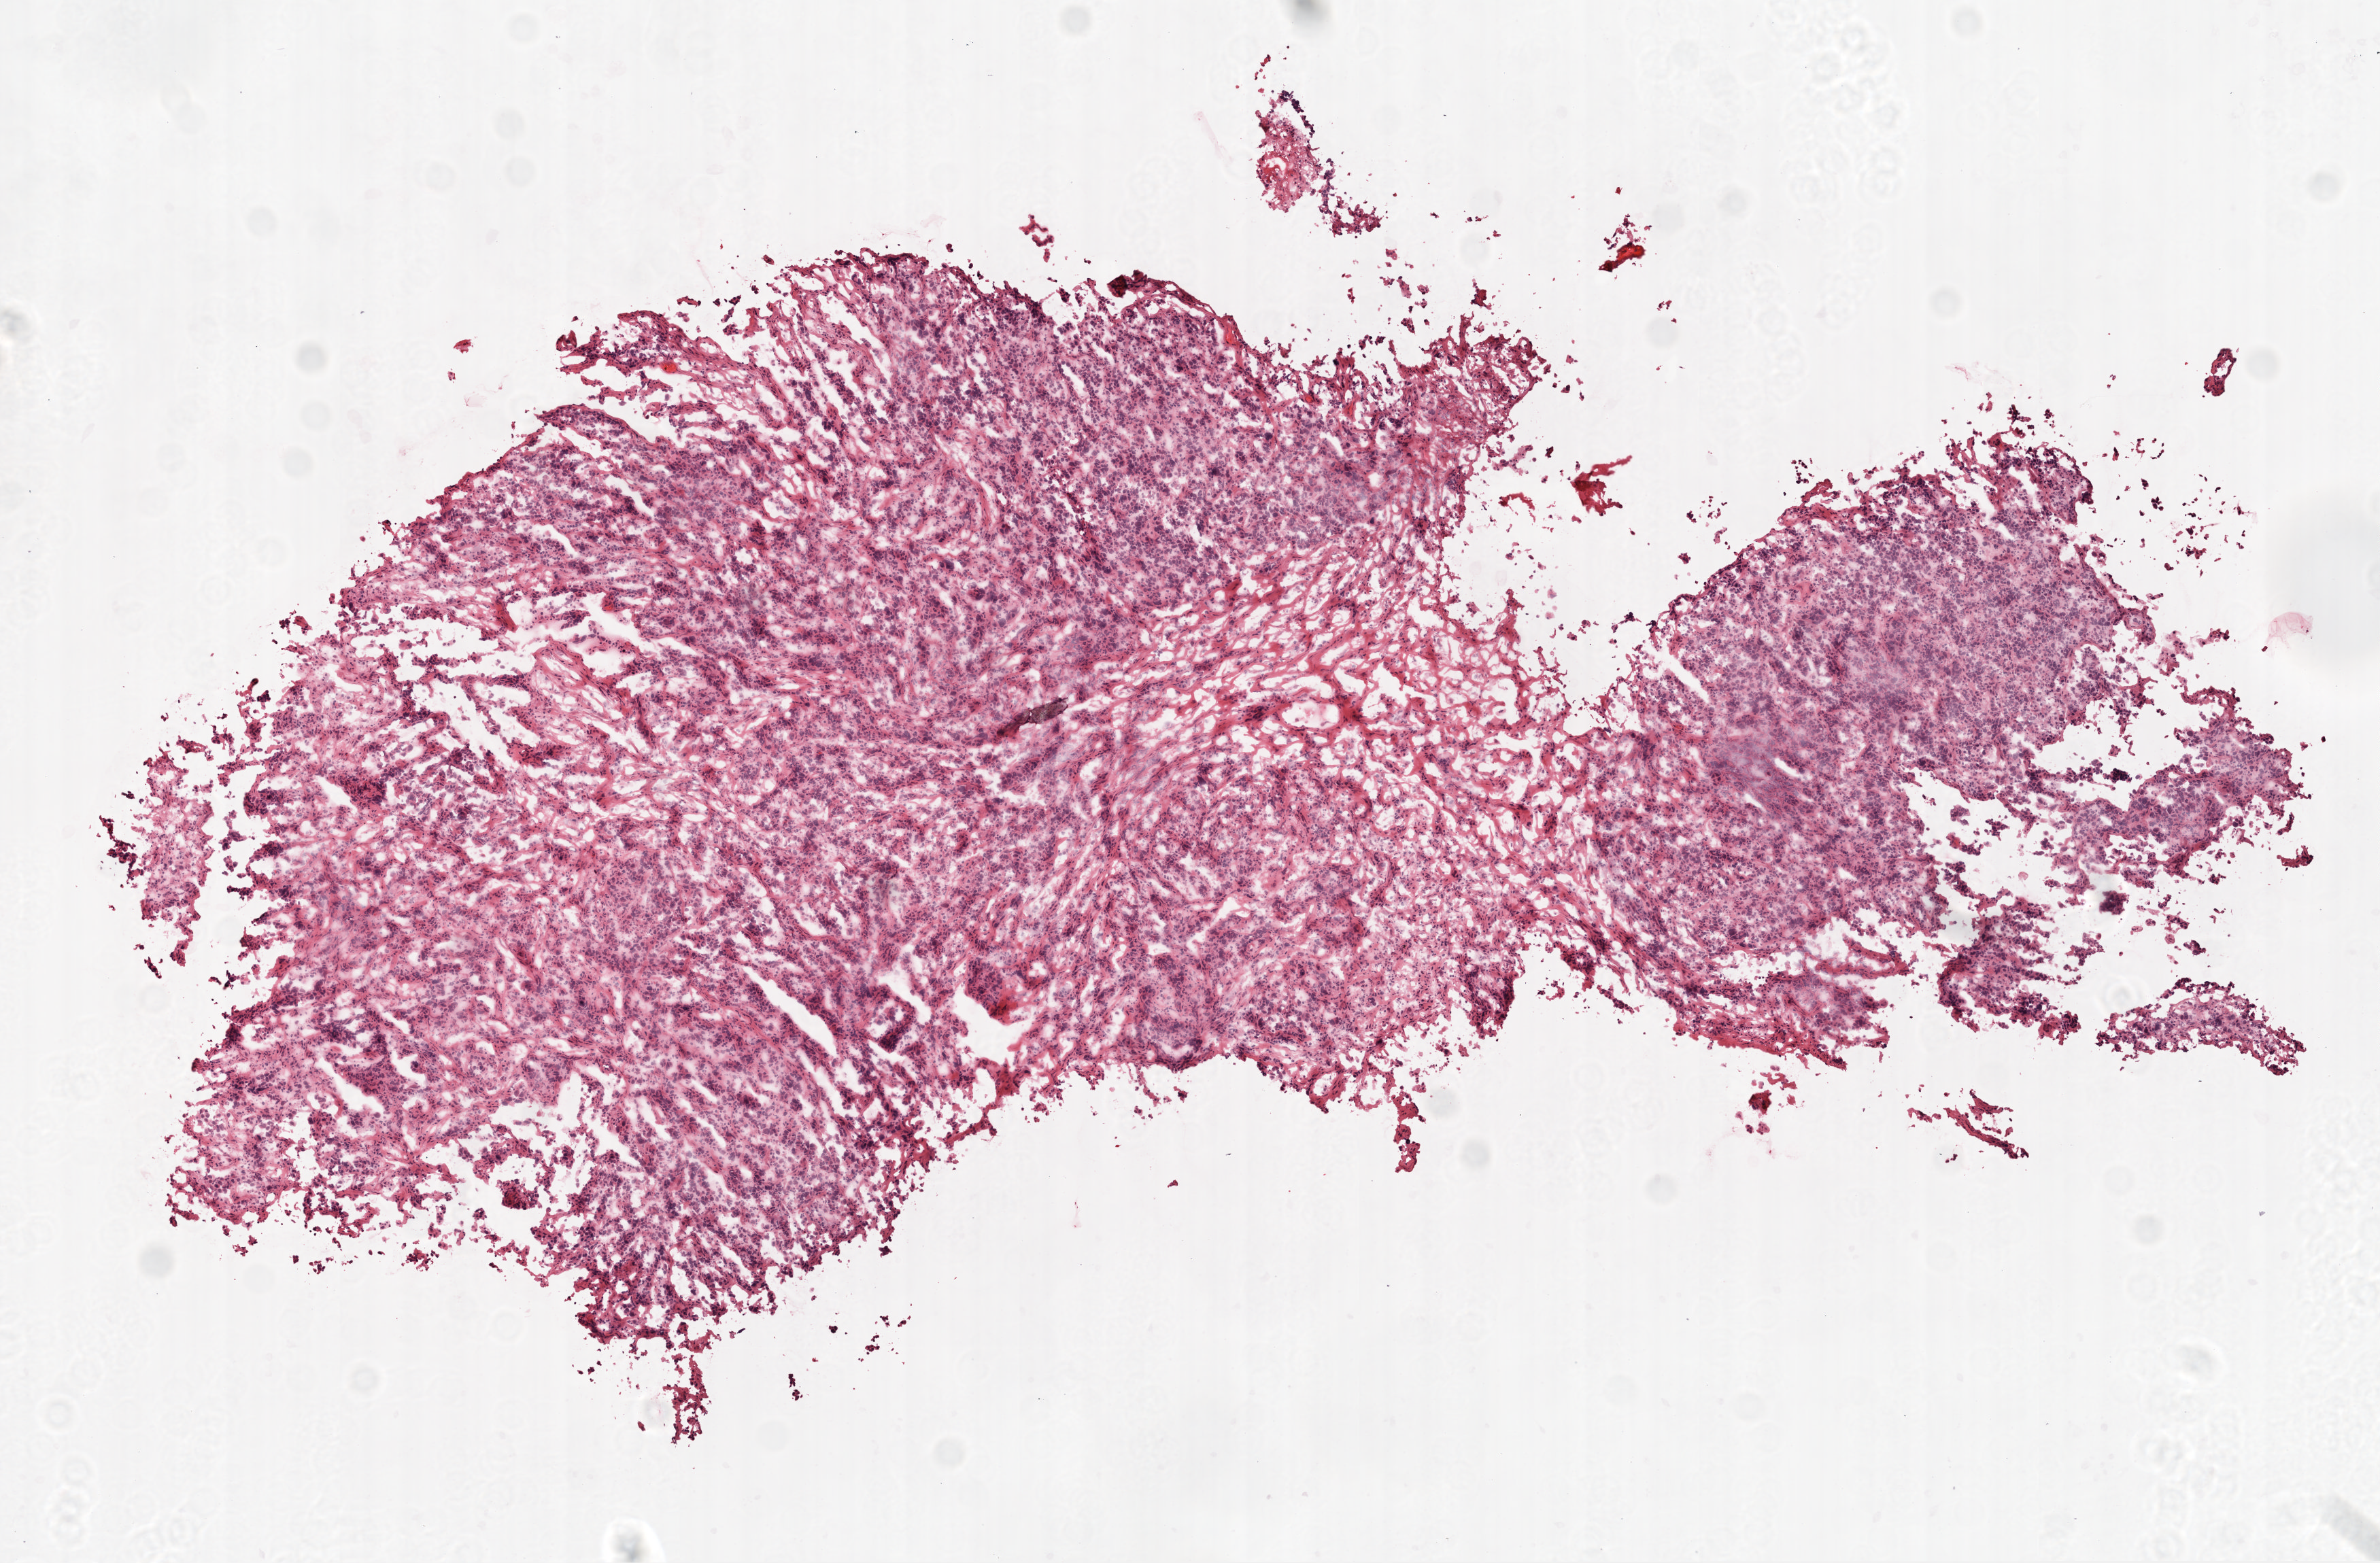
Whole-slide histology image, Hematoxylin and eosin (H&E) stained, shown as a low-resolution overview of the whole scanned area (about 7.0 x 4.6 mm, slide scanned at 20x), frozen section from the top of the tissue portion, primary tumour sample from the ovary. Female, age 78 years at initial diagnosis. Histologic grade: G3 (poorly differentiated). Pathologist review of this section (percent, as recorded): tumour cells 99%, tumour nuclei 99%, normal cells 0%, stromal cells 1%, necrosis 0%.
Diagnosis: Serous cystadenocarcinoma, NOS. FIGO stage: IV.